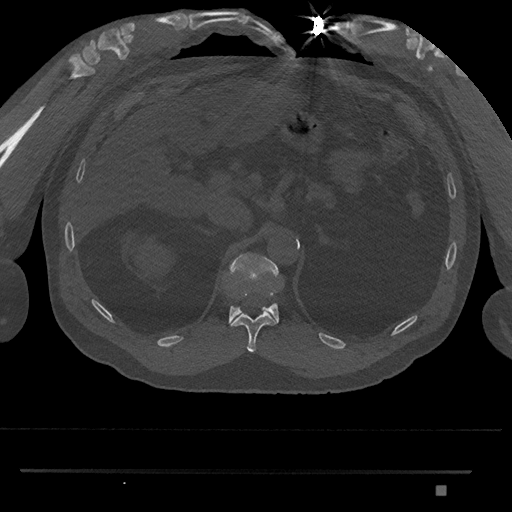
CT including the spine, one axial slice; position 922 of 1134 along the scan axis; 120 kVp; bone window (W 1800 / L 400 HU); 0.5 mm slice thickness; 512 × 512 image matrix, field of view 429 × 429 mm. Male patient, age 65 years. Case-level facts recorded for this patient, not image findings: primary cancer: prostate.
Outlined on this slice (semi-automatically segmented with operator editing):
- T11 vertebra: box from (x=230, y=294) to (x=277, y=353) px
- T12 vertebra: (x=228, y=252)–(x=279, y=324)